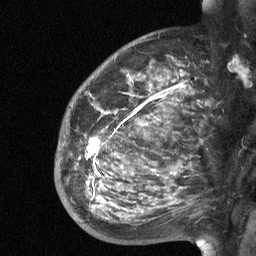
Breast MRI (dynamic contrast-enhanced), one sagittal slice; slice 45 of 64 in the series (ordered by position); dynamic contrast-enhanced study with each time point stored as its own series, time point 2 of 3 at this slice position (early post-contrast, ordered by acquisition time); 1.5 T; TE 4.8 ms, TR 27 ms; 256 × 256 image matrix, field of view 200 × 200 mm. Female patient, age 50 years. Case-level facts recorded for this patient, not image findings: setting: breast cancer imaged before/during neoadjuvant chemotherapy; receptor status: HER2-positive.
Annotated regions visible in this slice (semi-automatically segmented with operator editing):
- analysis volume of interest (the breast-tissue region the enhancement analysis was run in; not a lesion): bounding box [x1, y1, x2, y2] px = [55, 91, 203, 227]
- tumour enhancement mask (voxels above the 90 % enhancement threshold inside the analysis volume of interest): [87, 138, 104, 203]